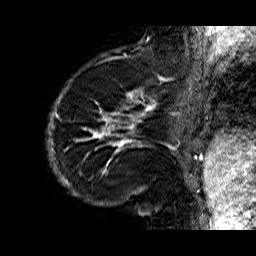
Breast MRI (dynamic contrast-enhanced), one sagittal slice; slice 9 of 60 in the series (ordered by position); dynamic contrast-enhanced series, time point 2 of 6 at this slice position (early post-contrast); 1.5 T; TE 6.3 ms, TR 32.9 ms; 4 mm slice thickness; 256 × 256 image matrix, field of view 200 × 200 mm. Female patient. From the clinical record (not read from this slice): setting: breast cancer imaged before/during neoadjuvant chemotherapy; receptor status: HR-positive, HER2-negative.
Annotated regions visible in this slice (semi-automatically segmented with operator editing):
- analysis volume of interest (the breast-tissue region the enhancement analysis was run in; not a lesion): bounding box [x1, y1, x2, y2] px = [47, 74, 176, 210]
- tumour enhancement mask (voxels above the 100 % enhancement threshold inside the analysis volume of interest): [47, 77, 176, 192]